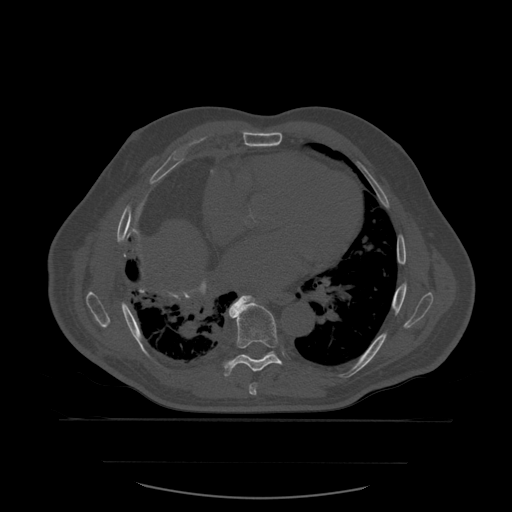
CT including the spine, one axial slice; slice 361 of 590 in the series (ordered by position); bone window (W 1800 / L 400 HU); 1.25 mm slice thickness; 512 × 512 image matrix. Patient age 71 years. From the clinical record (not read from this slice): primary cancer: lung.
Annotated regions visible in this slice (semi-automatic segmentation, software-assisted and operator-edited):
- T7 vertebra: bounding box (x1, y1, x2, y2) in pixels: (250, 383, 258, 396)
- T8 vertebra: (224, 296, 283, 377)
- T9 vertebra: (266, 352, 272, 356)